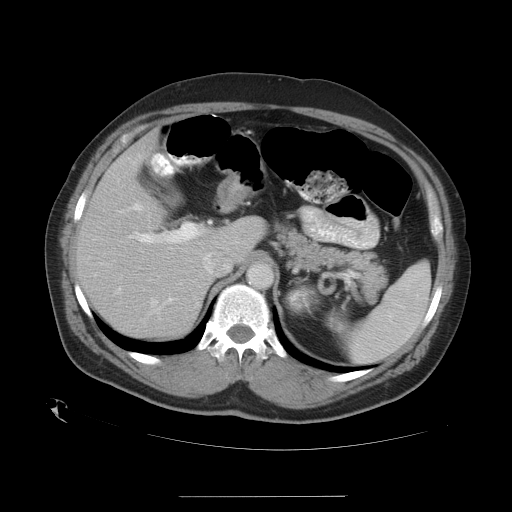
Contrast-enhanced abdominal CT, one axial slice. Position 21 of 35 along the scan axis. Intravenous contrast given. Soft-tissue window (W 400 / L 40 HU). 7.5 mm slice thickness. 512 × 512 image matrix, field of view 450 × 450 mm. Male patient, age 67 years. Case-level facts recorded for this patient, not image findings: diagnosis: colorectal cancer liver metastases, imaged before liver resection; multiple liver metastases: no.
Annotated regions visible in this slice (outlined manually by an expert reader):
- hepatic veins: bounding box [x1, y1, x2, y2] px = [117, 204, 157, 305]
- liver: [78, 139, 262, 338]
- planned liver remnant (the part of the liver to remain after resection): [84, 139, 263, 339]
- portal vein (with intrahepatic branches): [120, 211, 206, 257]